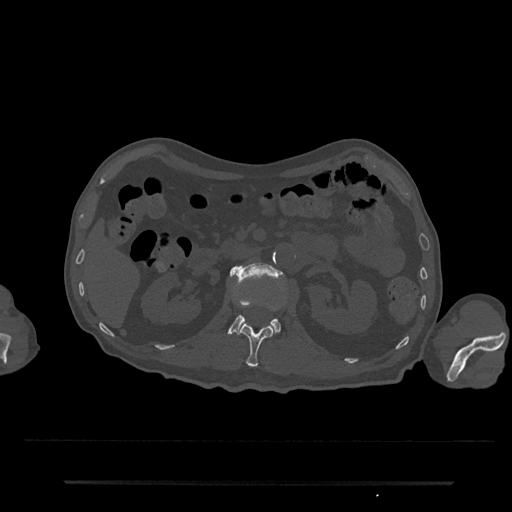
CT including the spine, one axial slice; position 101 of 797 along the scan axis; 120 kVp; bone window (W 1800 / L 400 HU); 0.5 mm slice thickness; 512 × 512 image matrix, field of view 427 × 427 mm. Patient: male, 74 years. Case-level facts recorded for this patient, not image findings: primary cancer: prostate.
Structures marked on this image (semi-automatic segmentation, software-assisted and operator-edited):
- L1 vertebra: bounding box [x1, y1, x2, y2] px = [240, 323, 274, 367]
- L2 vertebra: [228, 262, 282, 335]